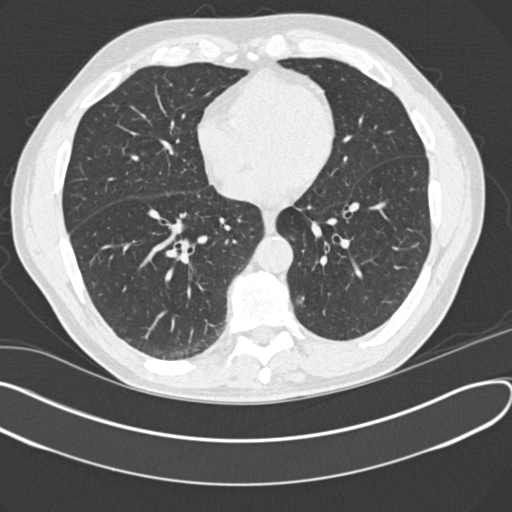
Axial slice from a low-dose chest CT screening exam; third annual screen; lung window (W 1500 / L -600 HU); 2 mm slice thickness. Male, age 64 years at enrolment. Former smoker at enrolment.
Expert reader's lesion annotation, bounding box (x1, y1, x2, y2) in pixels: (278, 282, 324, 321). Reader record for this screening exam (exam-level; its link to the box is not recorded): non-calcified nodule or mass ≥4 mm, left lower lobe, 8 × 7 mm, smooth margins, ground glass attenuation.